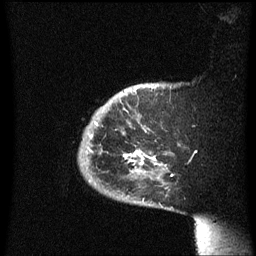
Breast MRI (dynamic contrast-enhanced), one sagittal slice; slice 51 of 60 in the series (ordered by position); dynamic contrast-enhanced series, image 2 of 3 at this slice position (ordered by acquisition); 1.5 T; TE 4.2 ms, TR 8.4 ms; 256 × 256 image matrix, field of view 200 × 200 mm. Female patient, age 38 years. Case-level facts recorded for this patient, not image findings: setting: breast cancer imaged before/during neoadjuvant chemotherapy; receptor status: HER2-positive.
Annotated regions visible in this slice (semi-automatic segmentation, software-assisted and operator-edited):
- analysis volume of interest (the breast-tissue region the enhancement analysis was run in; not a lesion): box from (x=78, y=84) to (x=187, y=211) px
- tumour enhancement mask (voxels above the 70 % enhancement threshold inside the analysis volume of interest): (x=91, y=136)–(x=161, y=173)